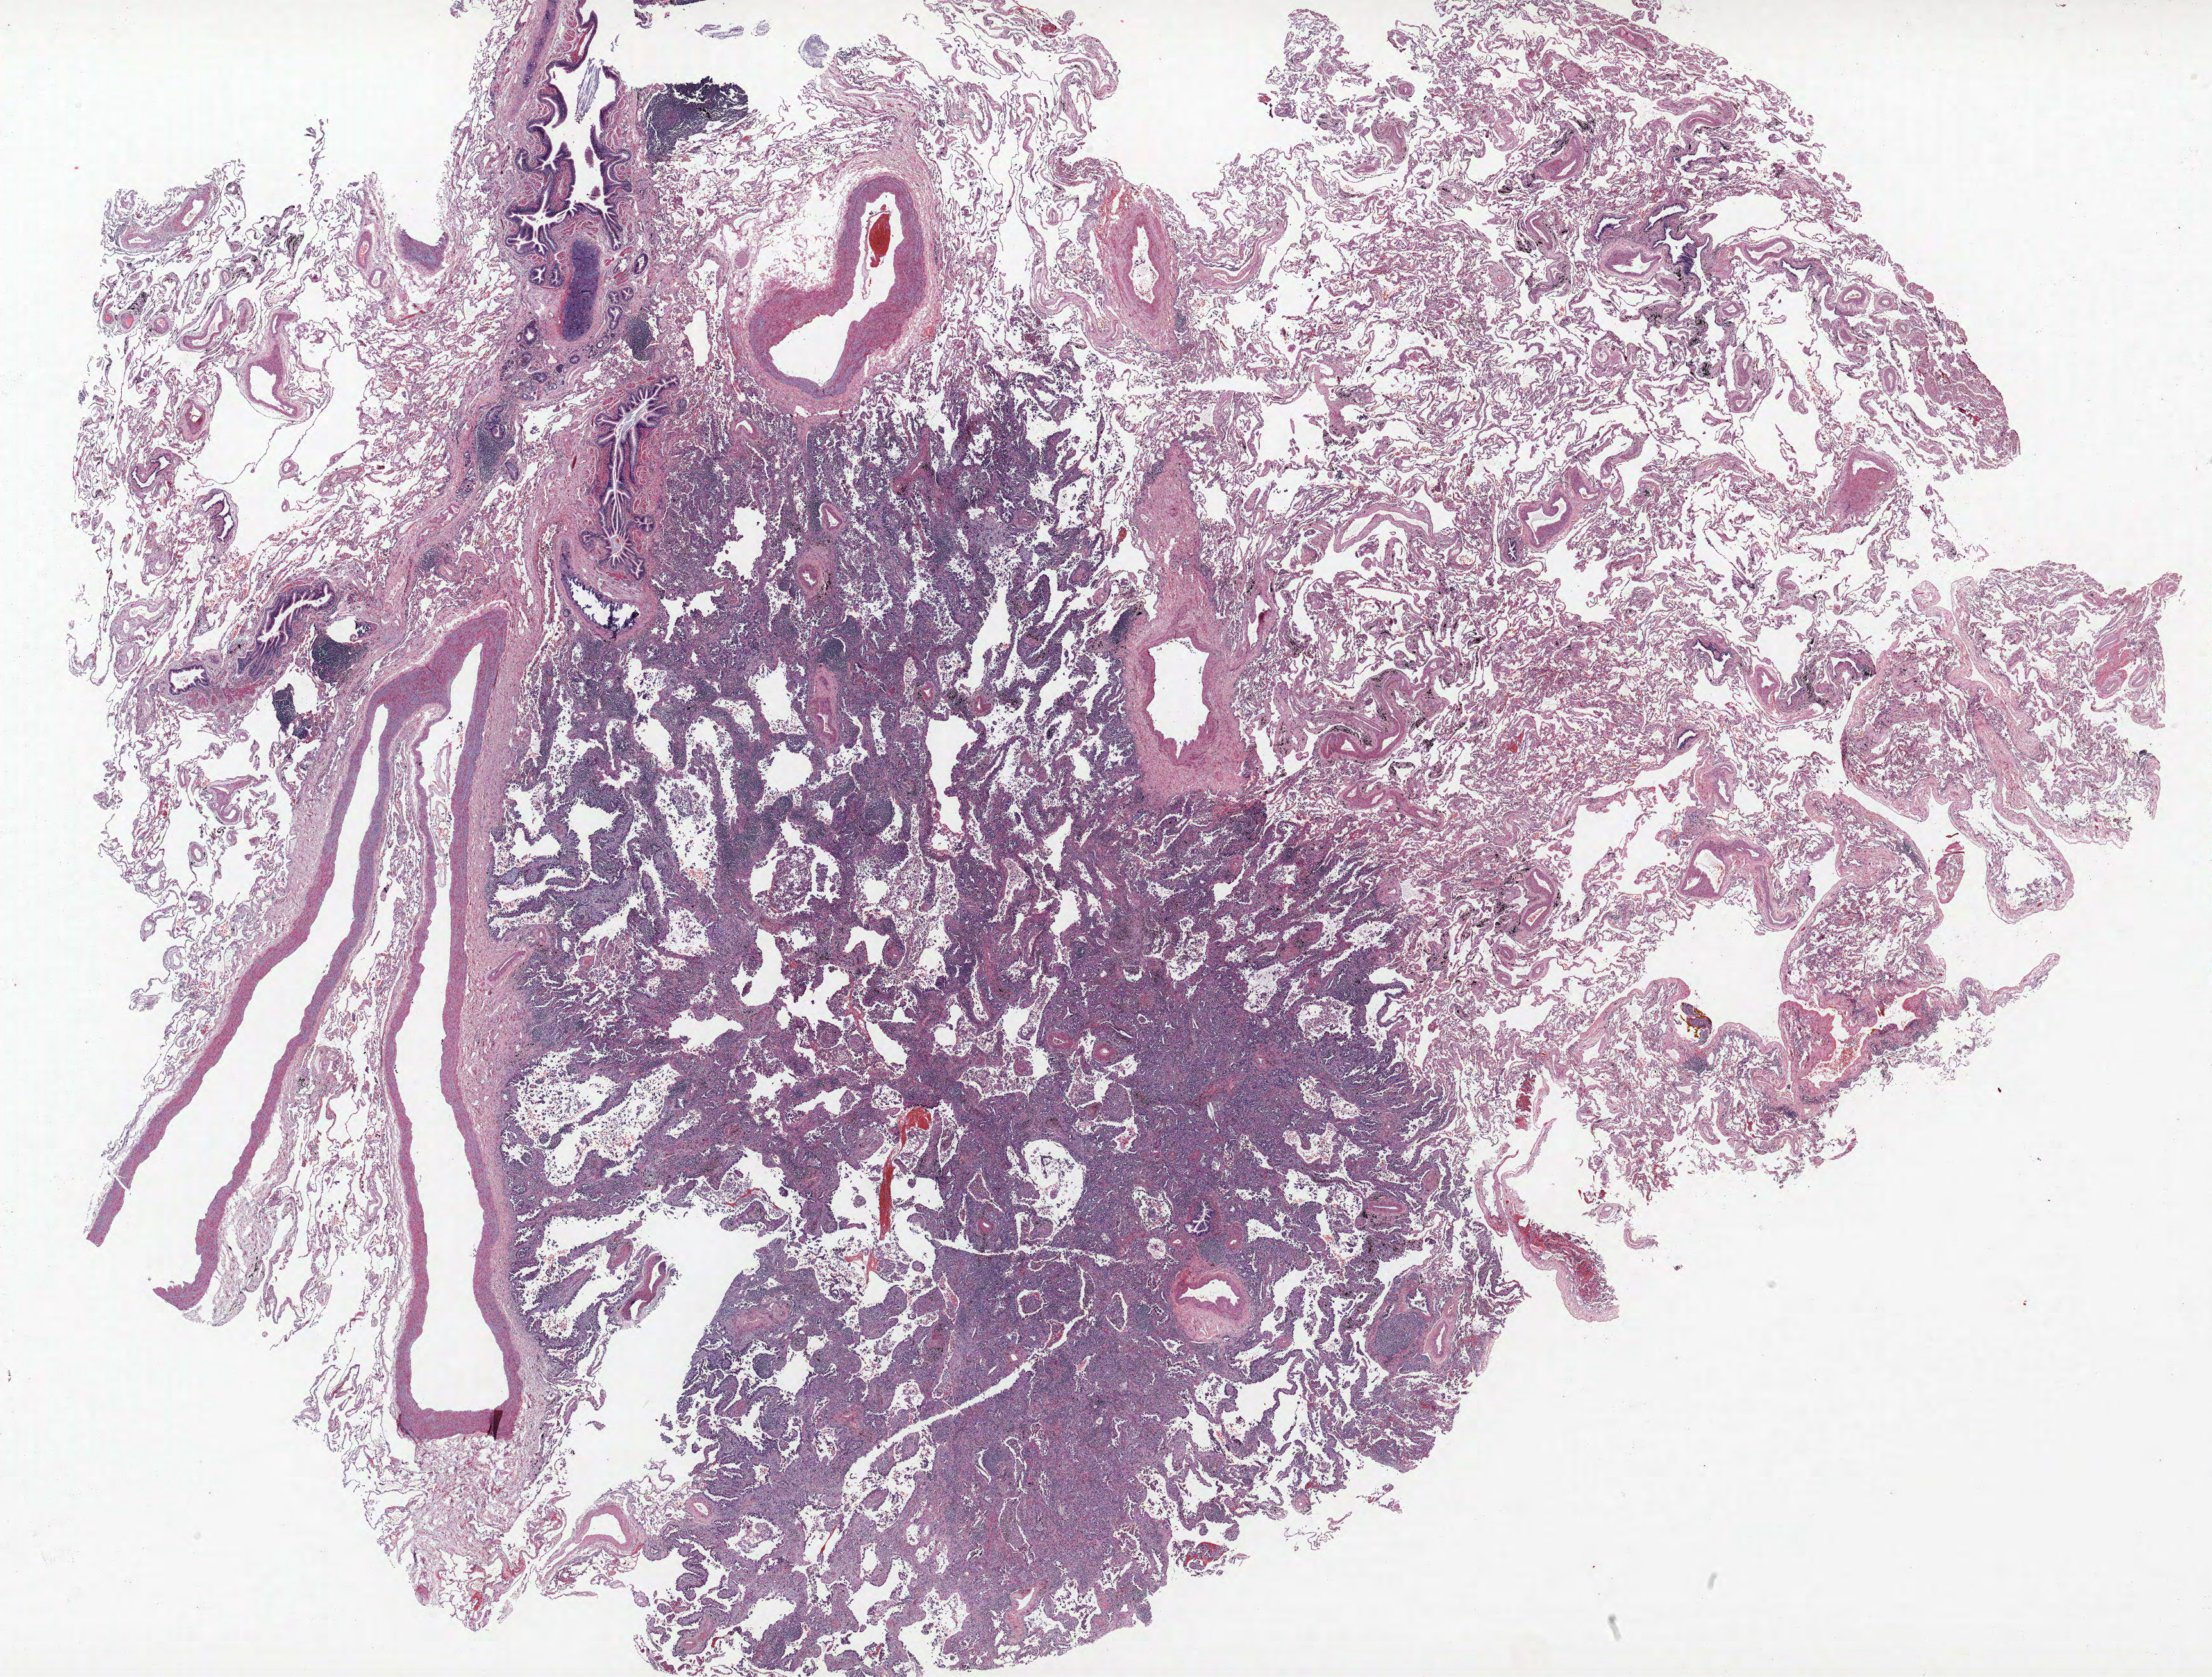
H&E-stained whole-slide image — low-resolution overview of the scanned area, about 27.6 x 20.9 mm (from a 40x scan). Formalin-fixed paraffin-embedded (FFPE) section. Lung tissue. Female, age 65 at enrolment. Grade: moderately differentiated (G2).
Participant's lung-cancer diagnosis: Adenocarcinoma, NOS. Primary tumour location (clinical record): right lower lobe. Stage (AJCC 6th edition): IA. Tumour size (pathology): 25 mm.